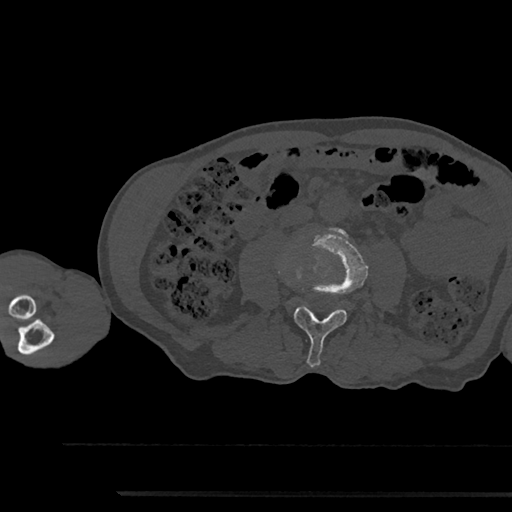
CT including the spine, one axial slice. Slice 464 of 797 in the series (ordered by position). Reconstruction kernel Br40s/3. Bone window (W 1800 / L 400 HU). 512 × 512 image matrix, field of view 367 × 367 mm. Male patient, age 79 years. From the clinical record (not read from this slice): primary cancer: prostate.
Annotated regions visible in this slice (semi-automatically segmented with operator editing):
- L3 vertebra: bounding box <287,228,367,367> (left, top, right, bottom; pixels)